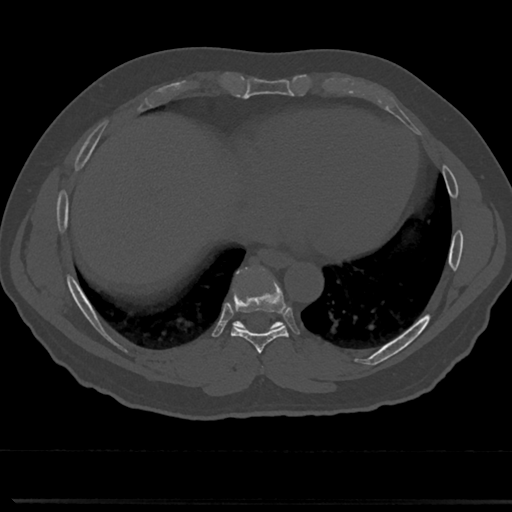
CT including the spine, one axial slice. Reconstruction kernel Br40s/3. Bone window (W 1800 / L 400 HU). 0.5 mm slice thickness. 512 × 512 image matrix, field of view 355 × 355 mm. Male patient, age 61 years. Case-level facts recorded for this patient, not image findings: primary cancer: prostate.
Annotated regions visible in this slice (semi-automatically segmented with operator editing):
- T7 vertebra: bounding box [x1, y1, x2, y2] px = [256, 342, 268, 377]
- T8 vertebra: [214, 271, 306, 354]